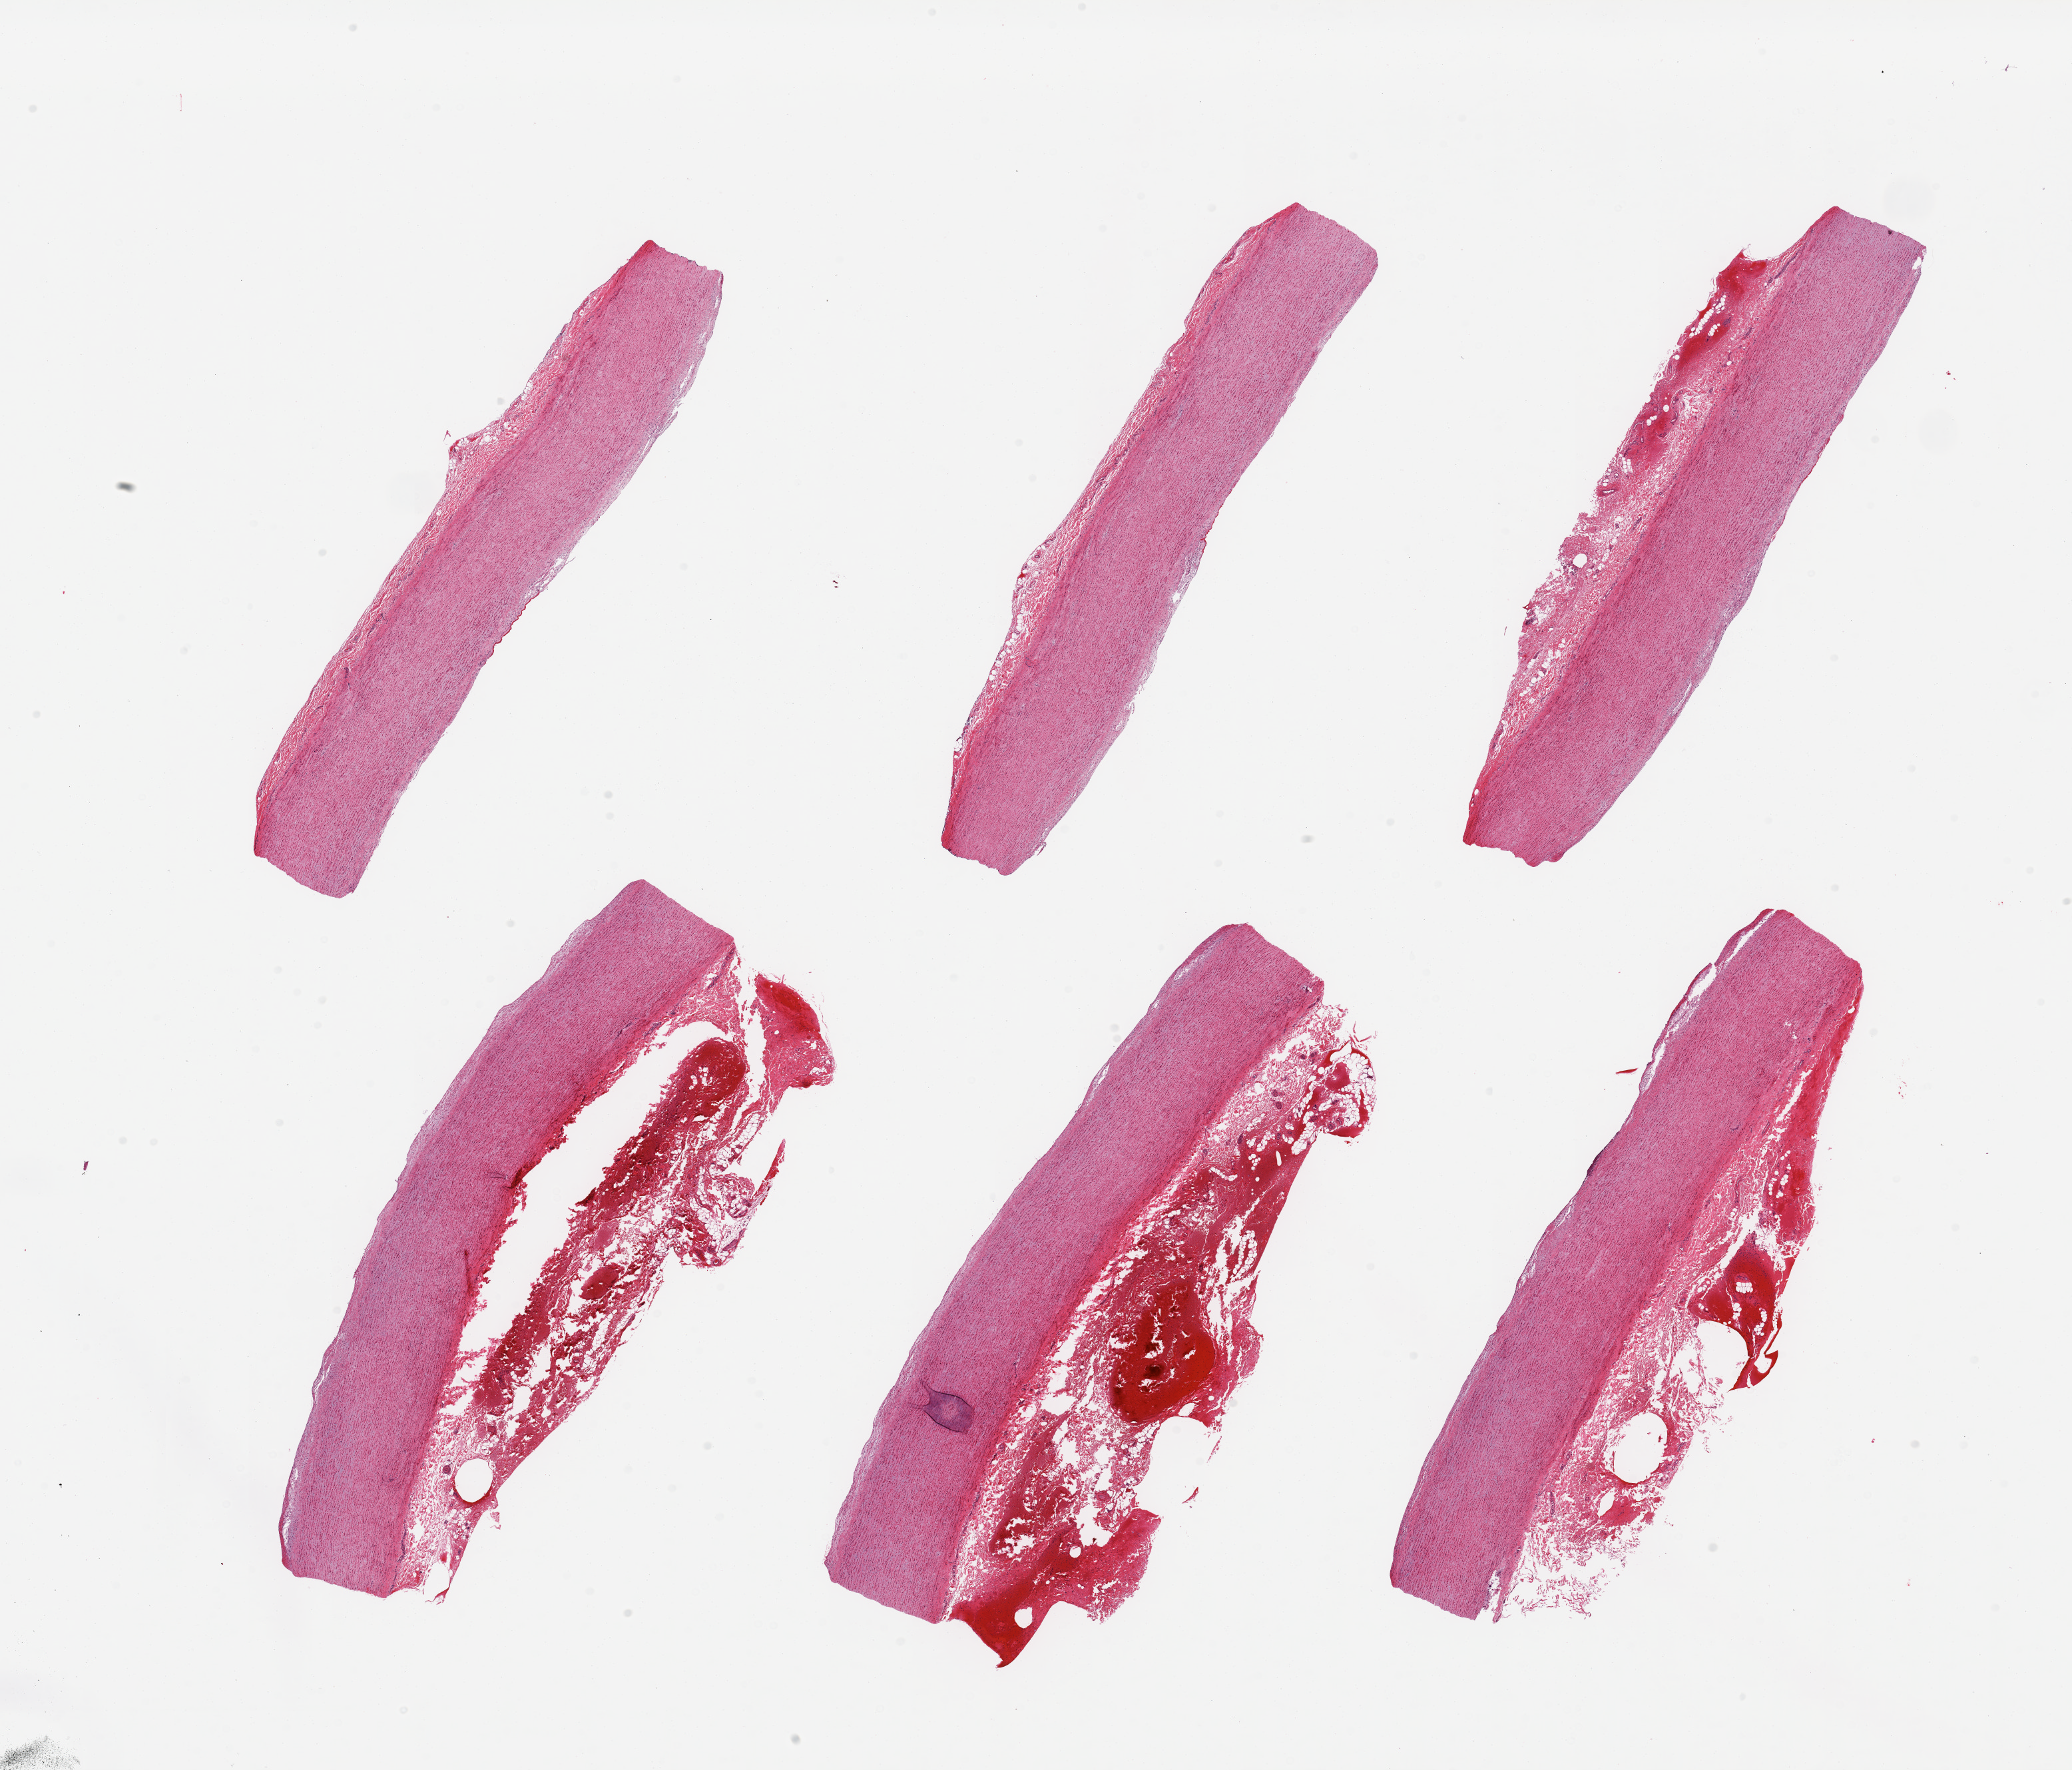
Digitized hematoxylin and eosin (H&E)-stained section, a low-resolution overview of the entire scanned area, about 24.6 x 21.0 mm. PAXgene-fixed paraffin-embedded (PFPE) section. Section of aorta (target tissue). Tissue donor sample. Donor: female.
Pathologist's review note for this sample: 6 pieces; minimal plaque; 4 pieces have hemorrhage in adventitia up to 2mm thick.